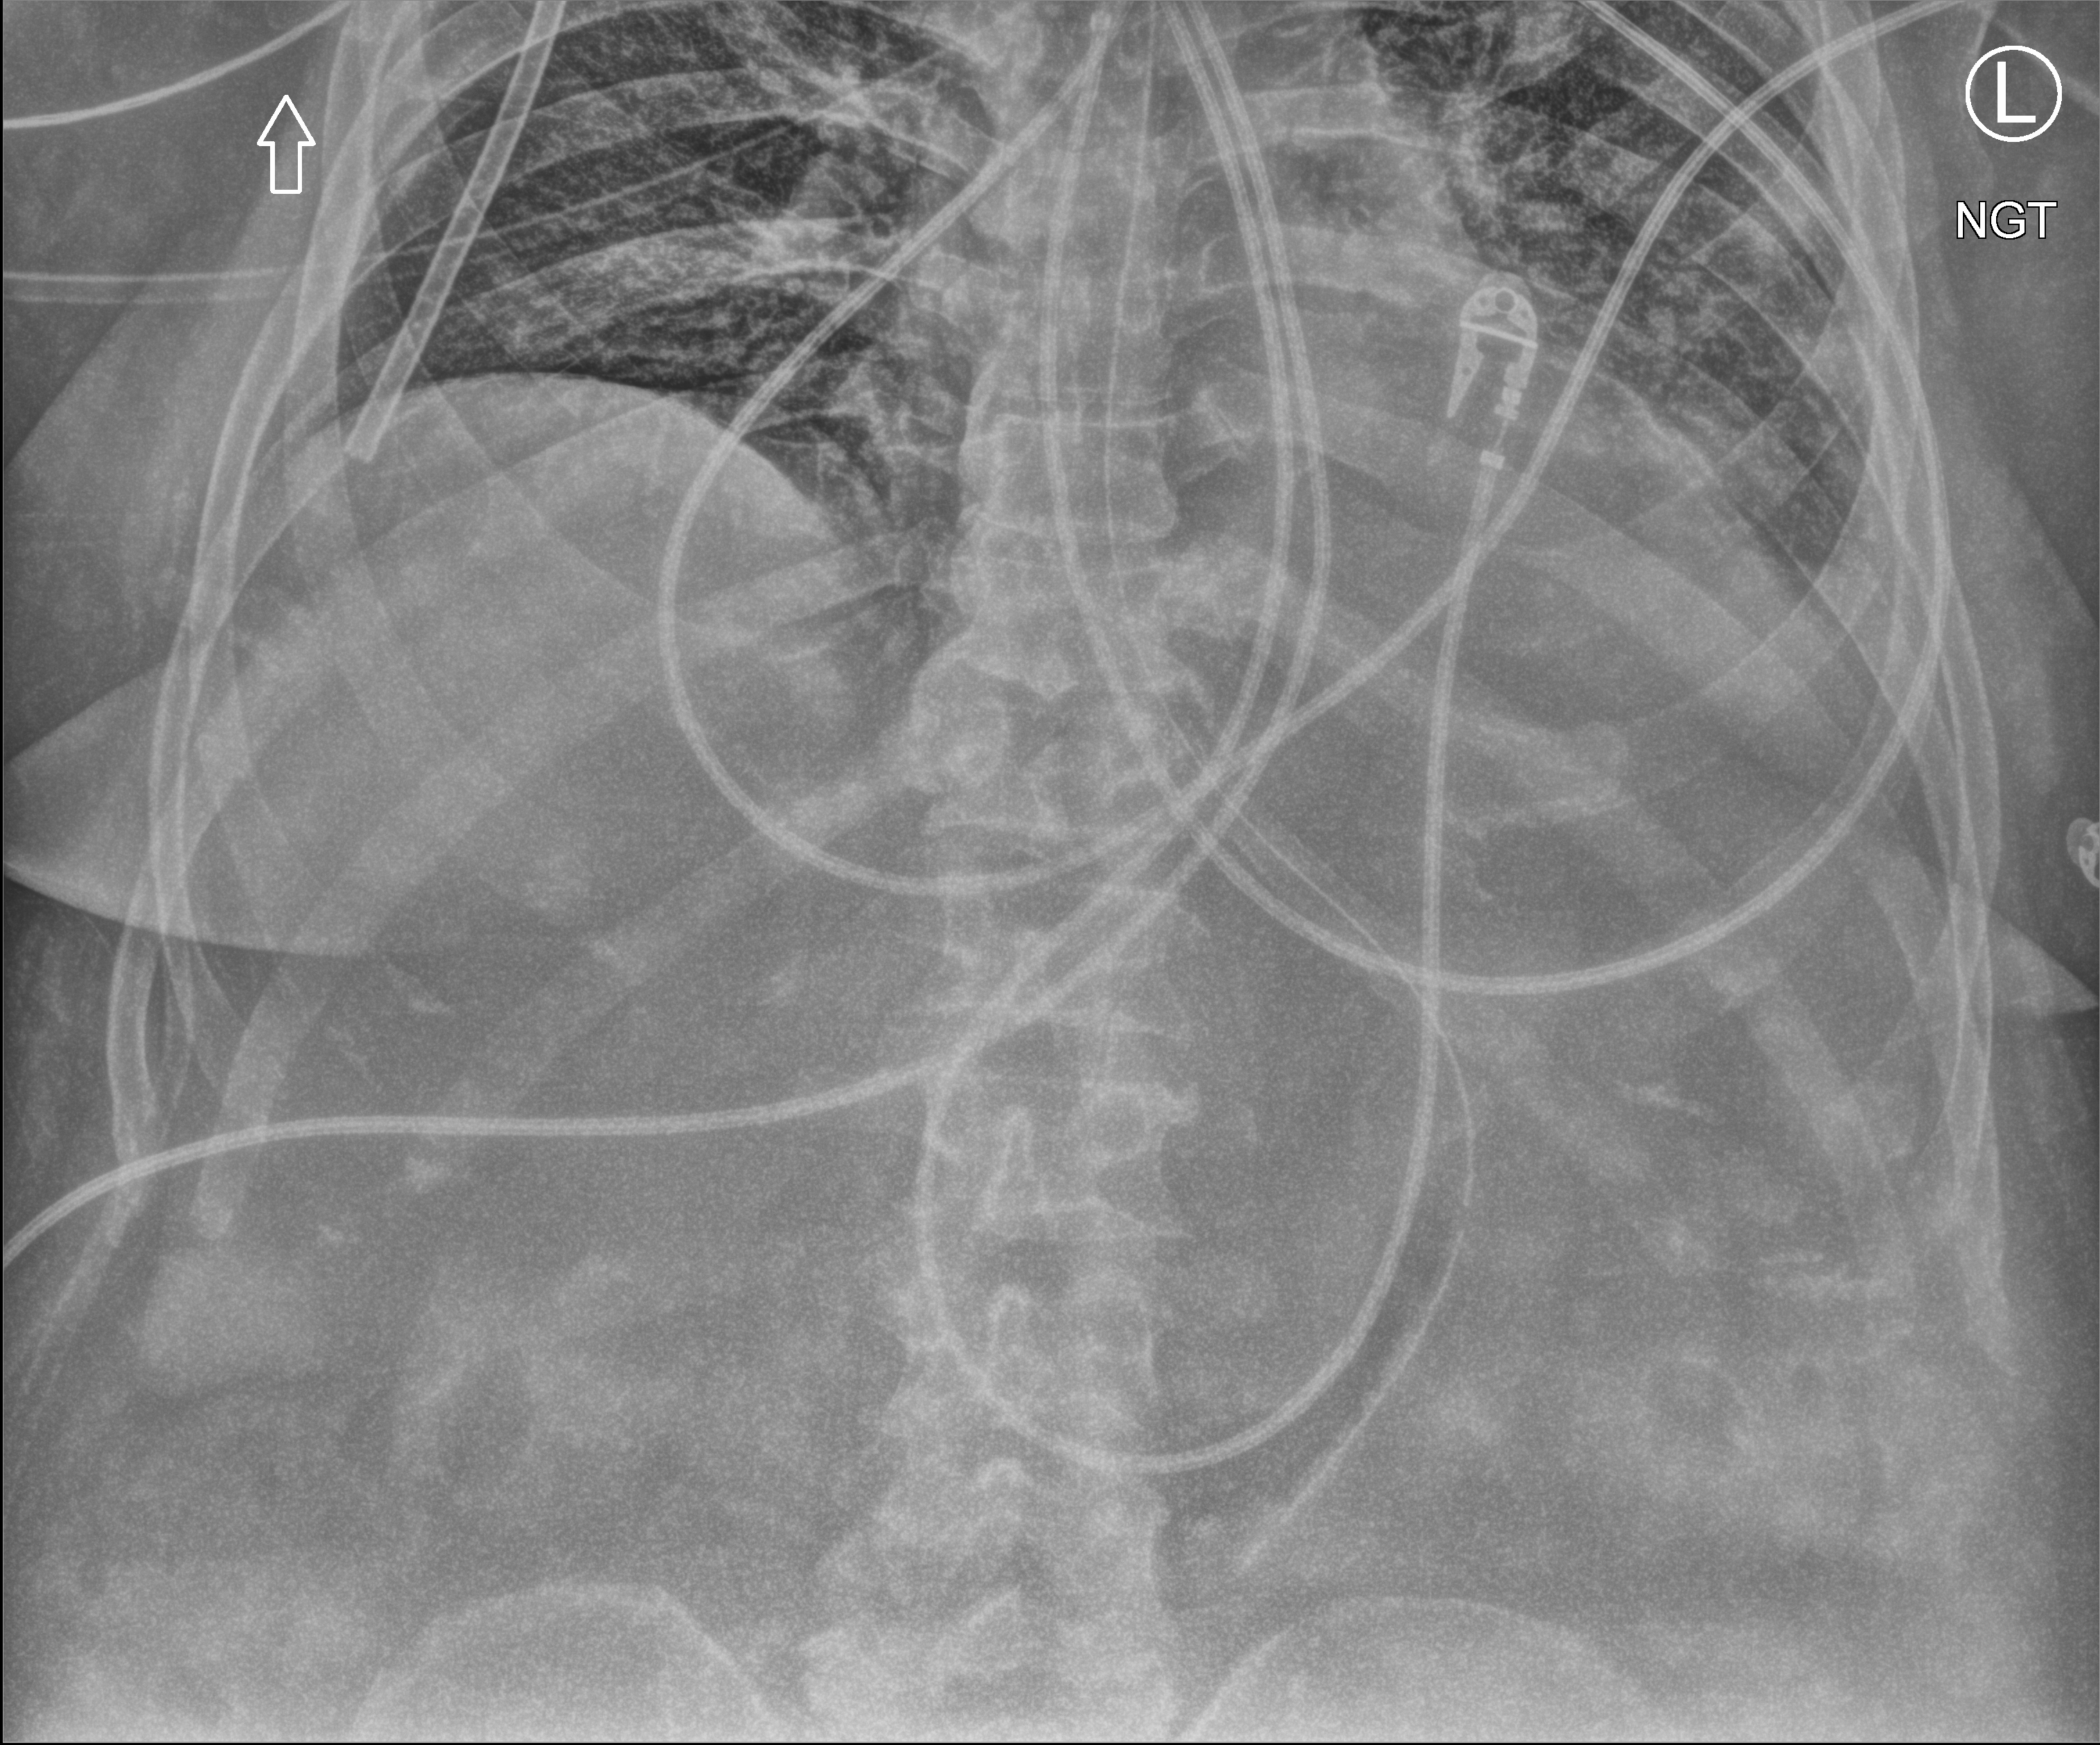
Abdomen radiograph, anteroposterior (AP) projection. Male patient hospitalised with COVID-19, age 60–74 years.
From the hospital-stay record, not from the radiograph (when in the stay this image was taken is not recorded): mechanically ventilated during this hospital stay: yes.